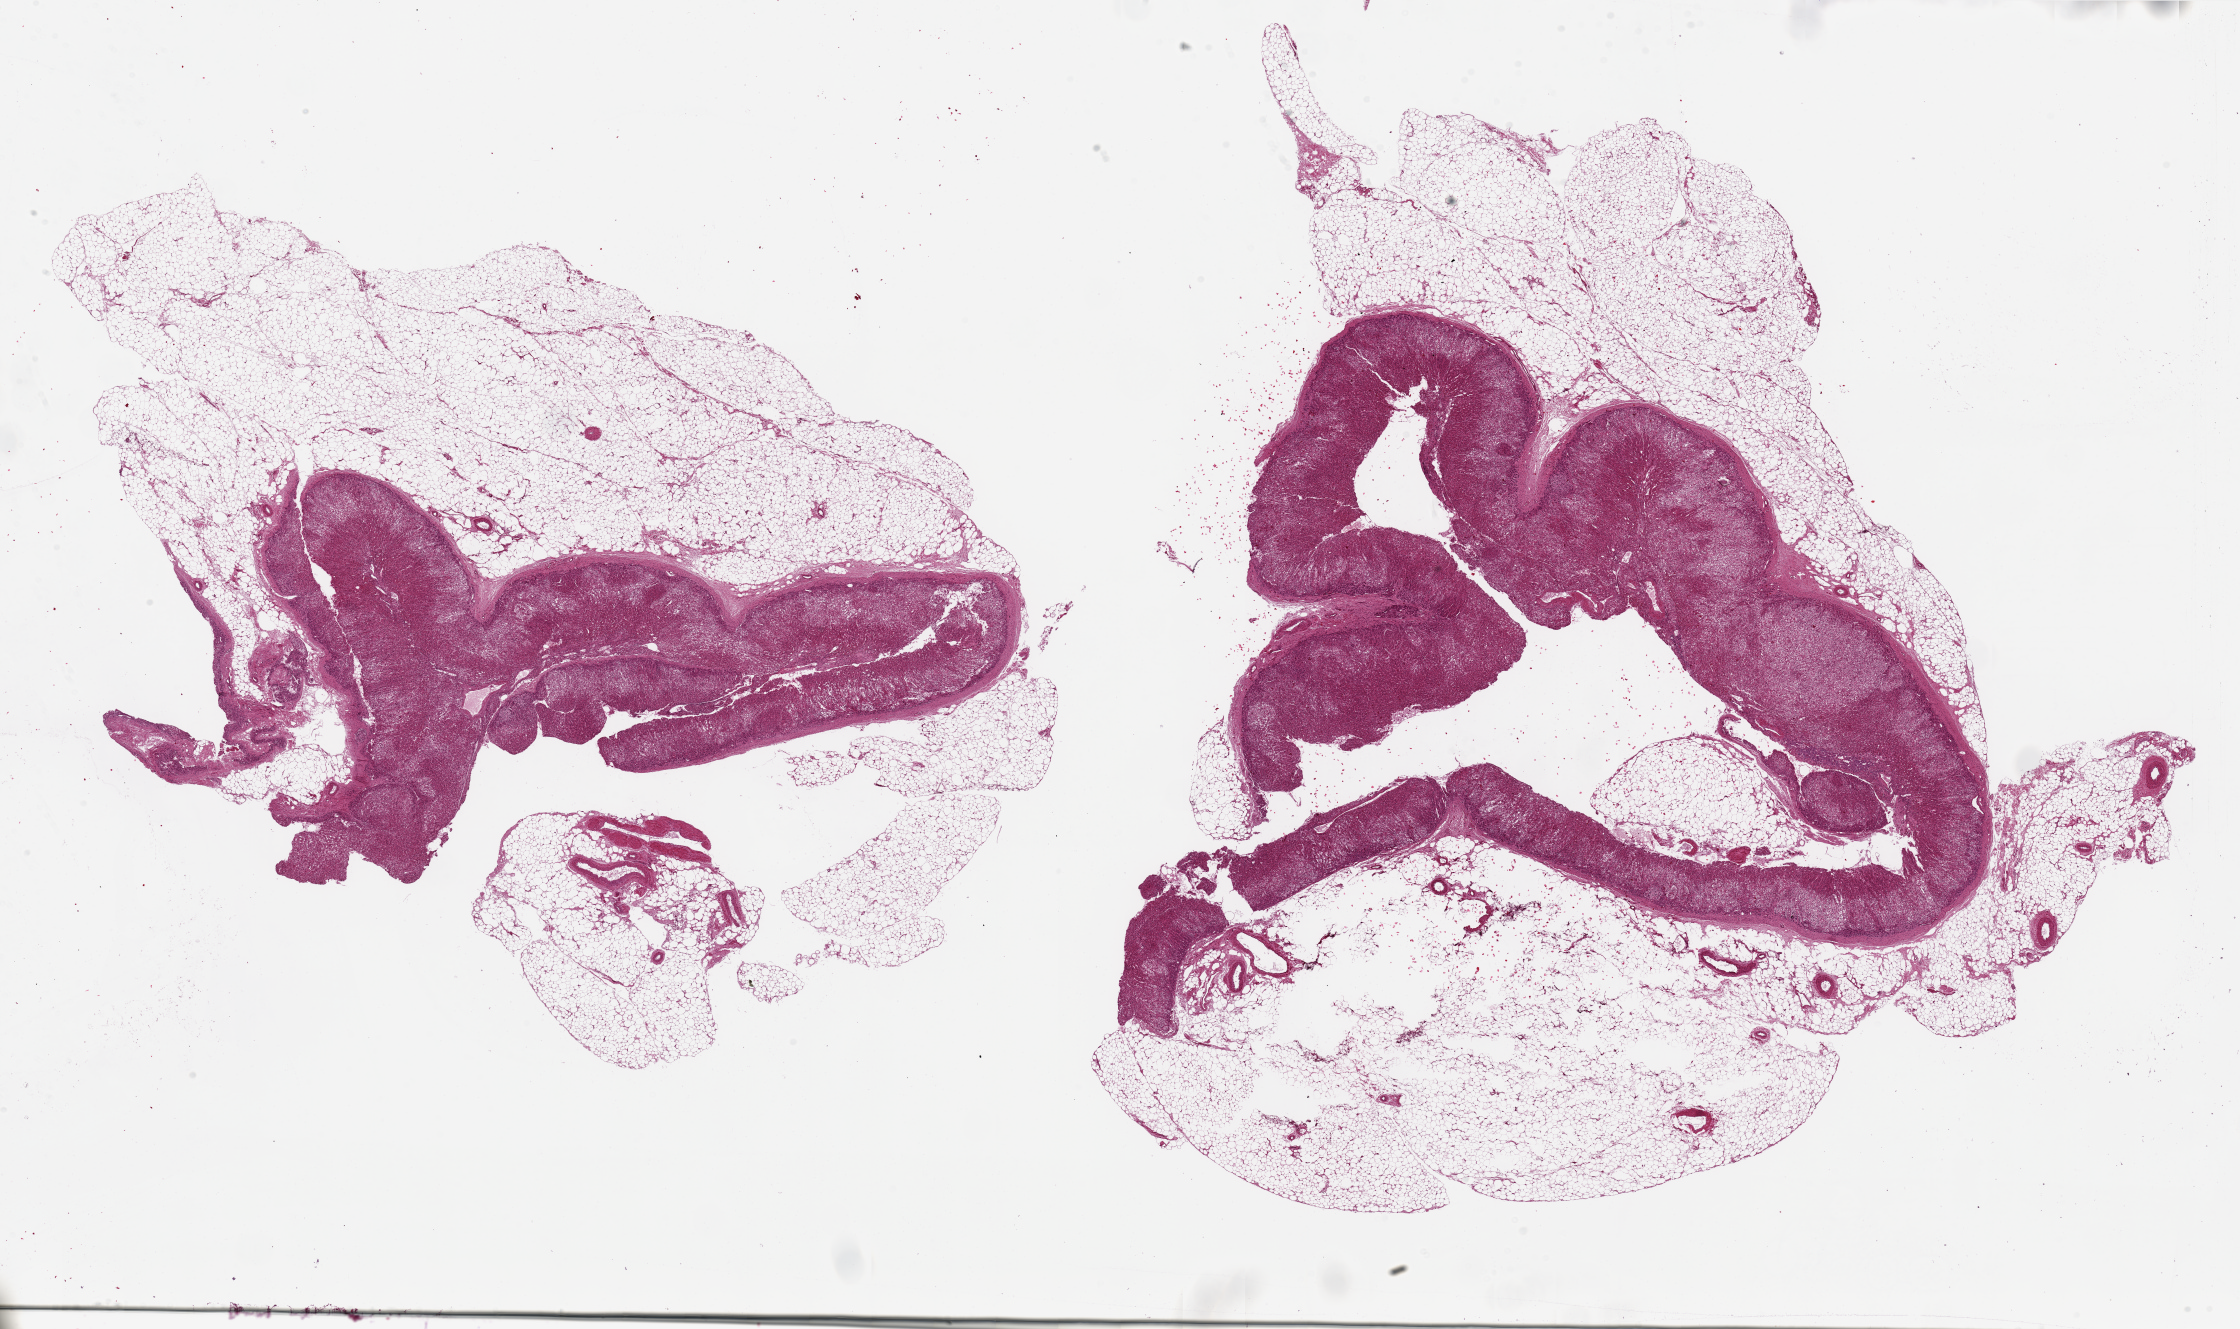
Digitized hematoxylin and eosin (H&E)-stained section — shown as a low-resolution overview of the whole scanned area (about 35.4 x 21.0 mm); PAXgene-fixed, paraffin-embedded tissue; section of adrenal gland (target tissue); donor tissue sample. Donor: male.
* pathologist's review note for this sample: 2 pieces, 18x11 & 19x17mm; both encased in adipose up to 50% of area